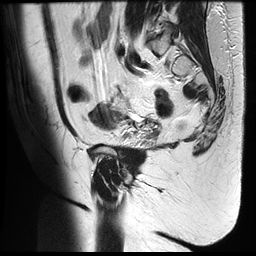
Pelvic MRI for cervical cancer, one sagittal slice; slice 10 of 35 in the series (ordered by position); T2-weighted; 1.5 T; TE 122.8 ms, TR 4992 ms; 4 mm slice thickness; 256 × 256 image matrix. Patient: female, 42 years.
Outlined on this slice (manually delineated by an expert):
- uterus and cervix: bounding box <88,102,159,138> (left, top, right, bottom; pixels)